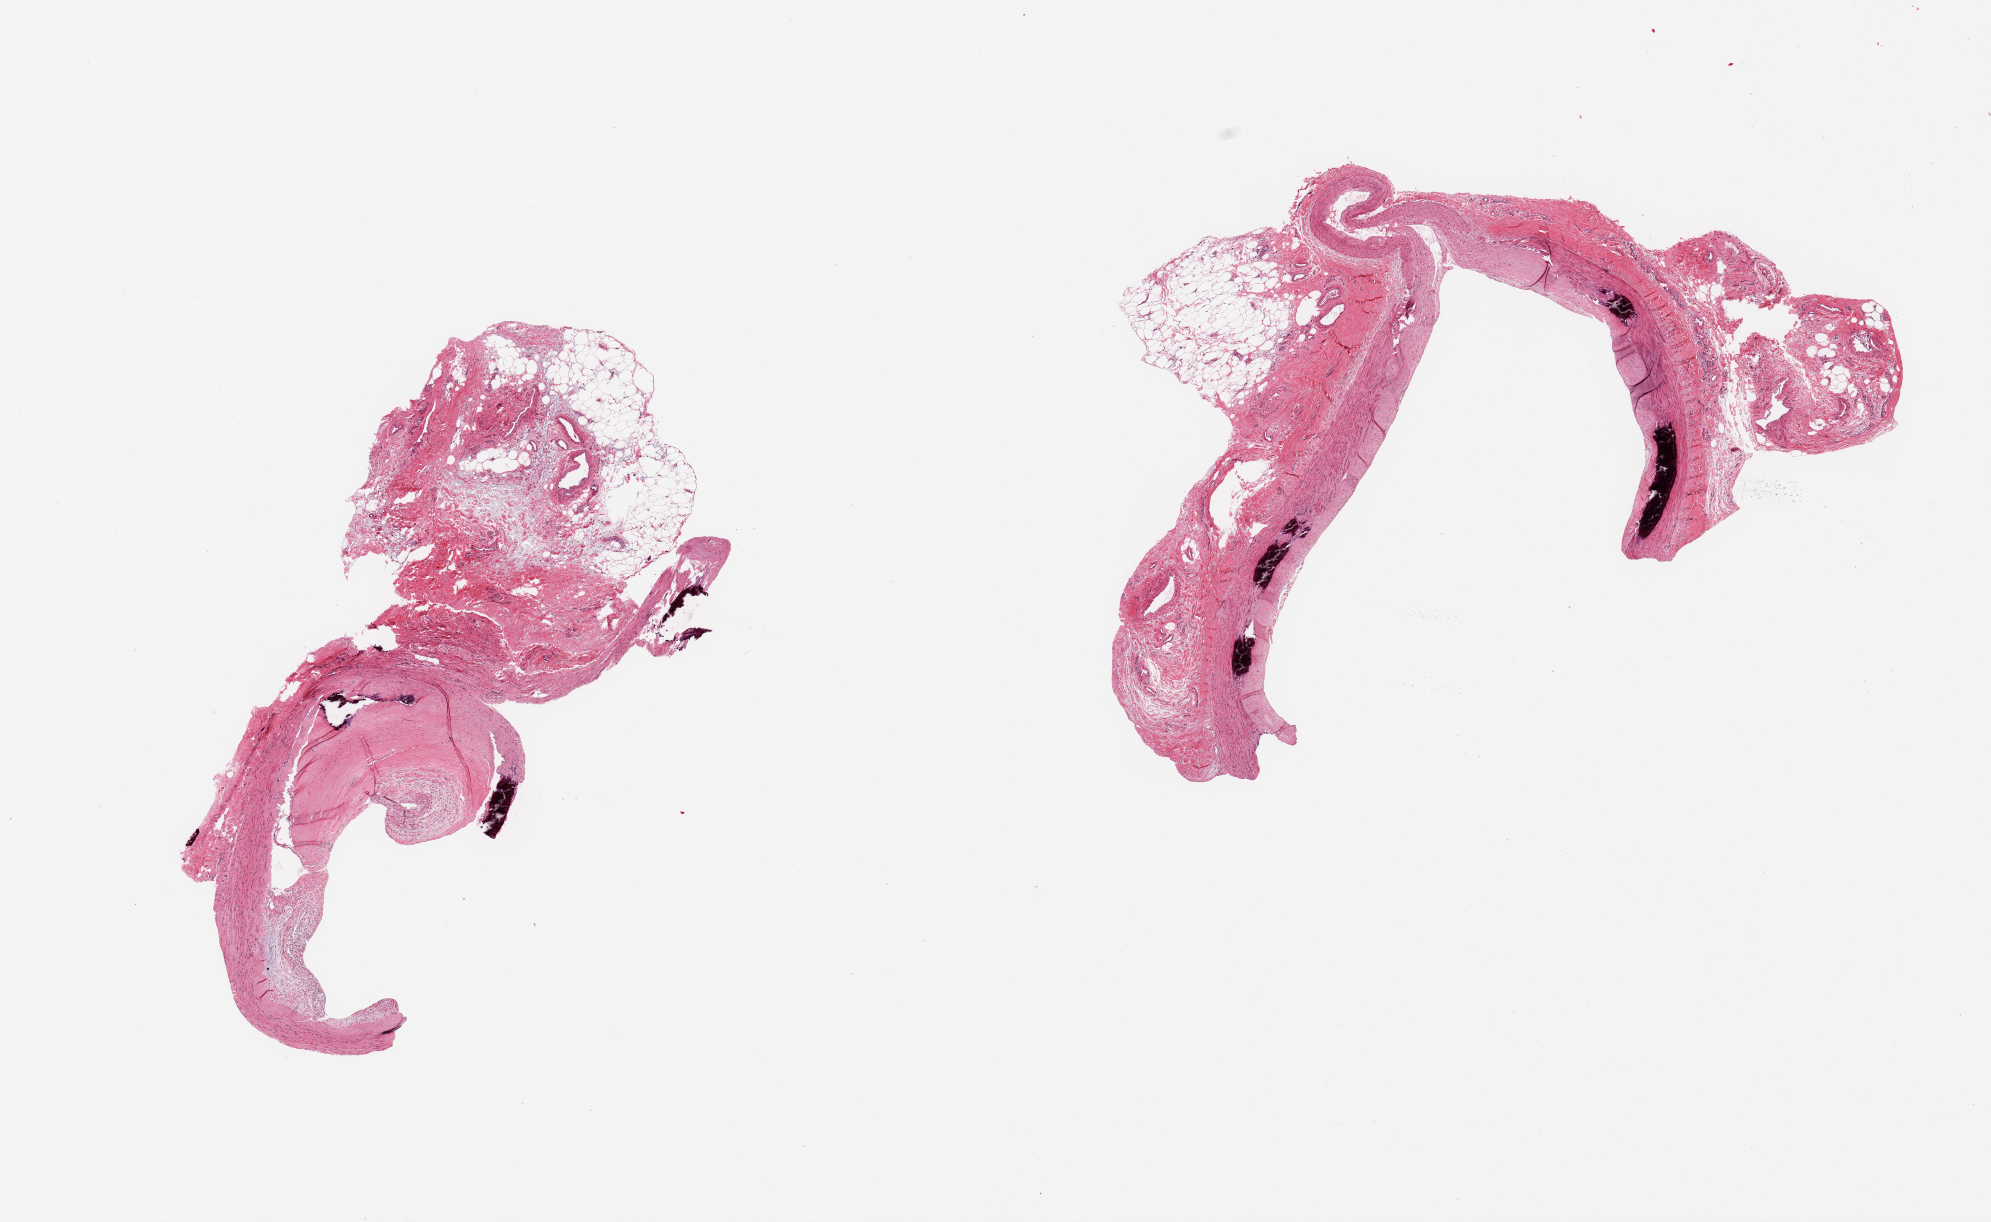
Digitized H&E-stained section, brightfield — whole scanned area (about 15.8 x 9.7 mm) shown as a low-resolution overview; PAXgene-fixed, paraffin-embedded tissue; section of tibial artery (target tissue); tissue donor sample. Male donor.
* review note (as recorded): 2 pieces; medial calcific sclerosis in both; large atherosclerotic plaque in one; fibrofatty external deposits up to 2.4 mm on each